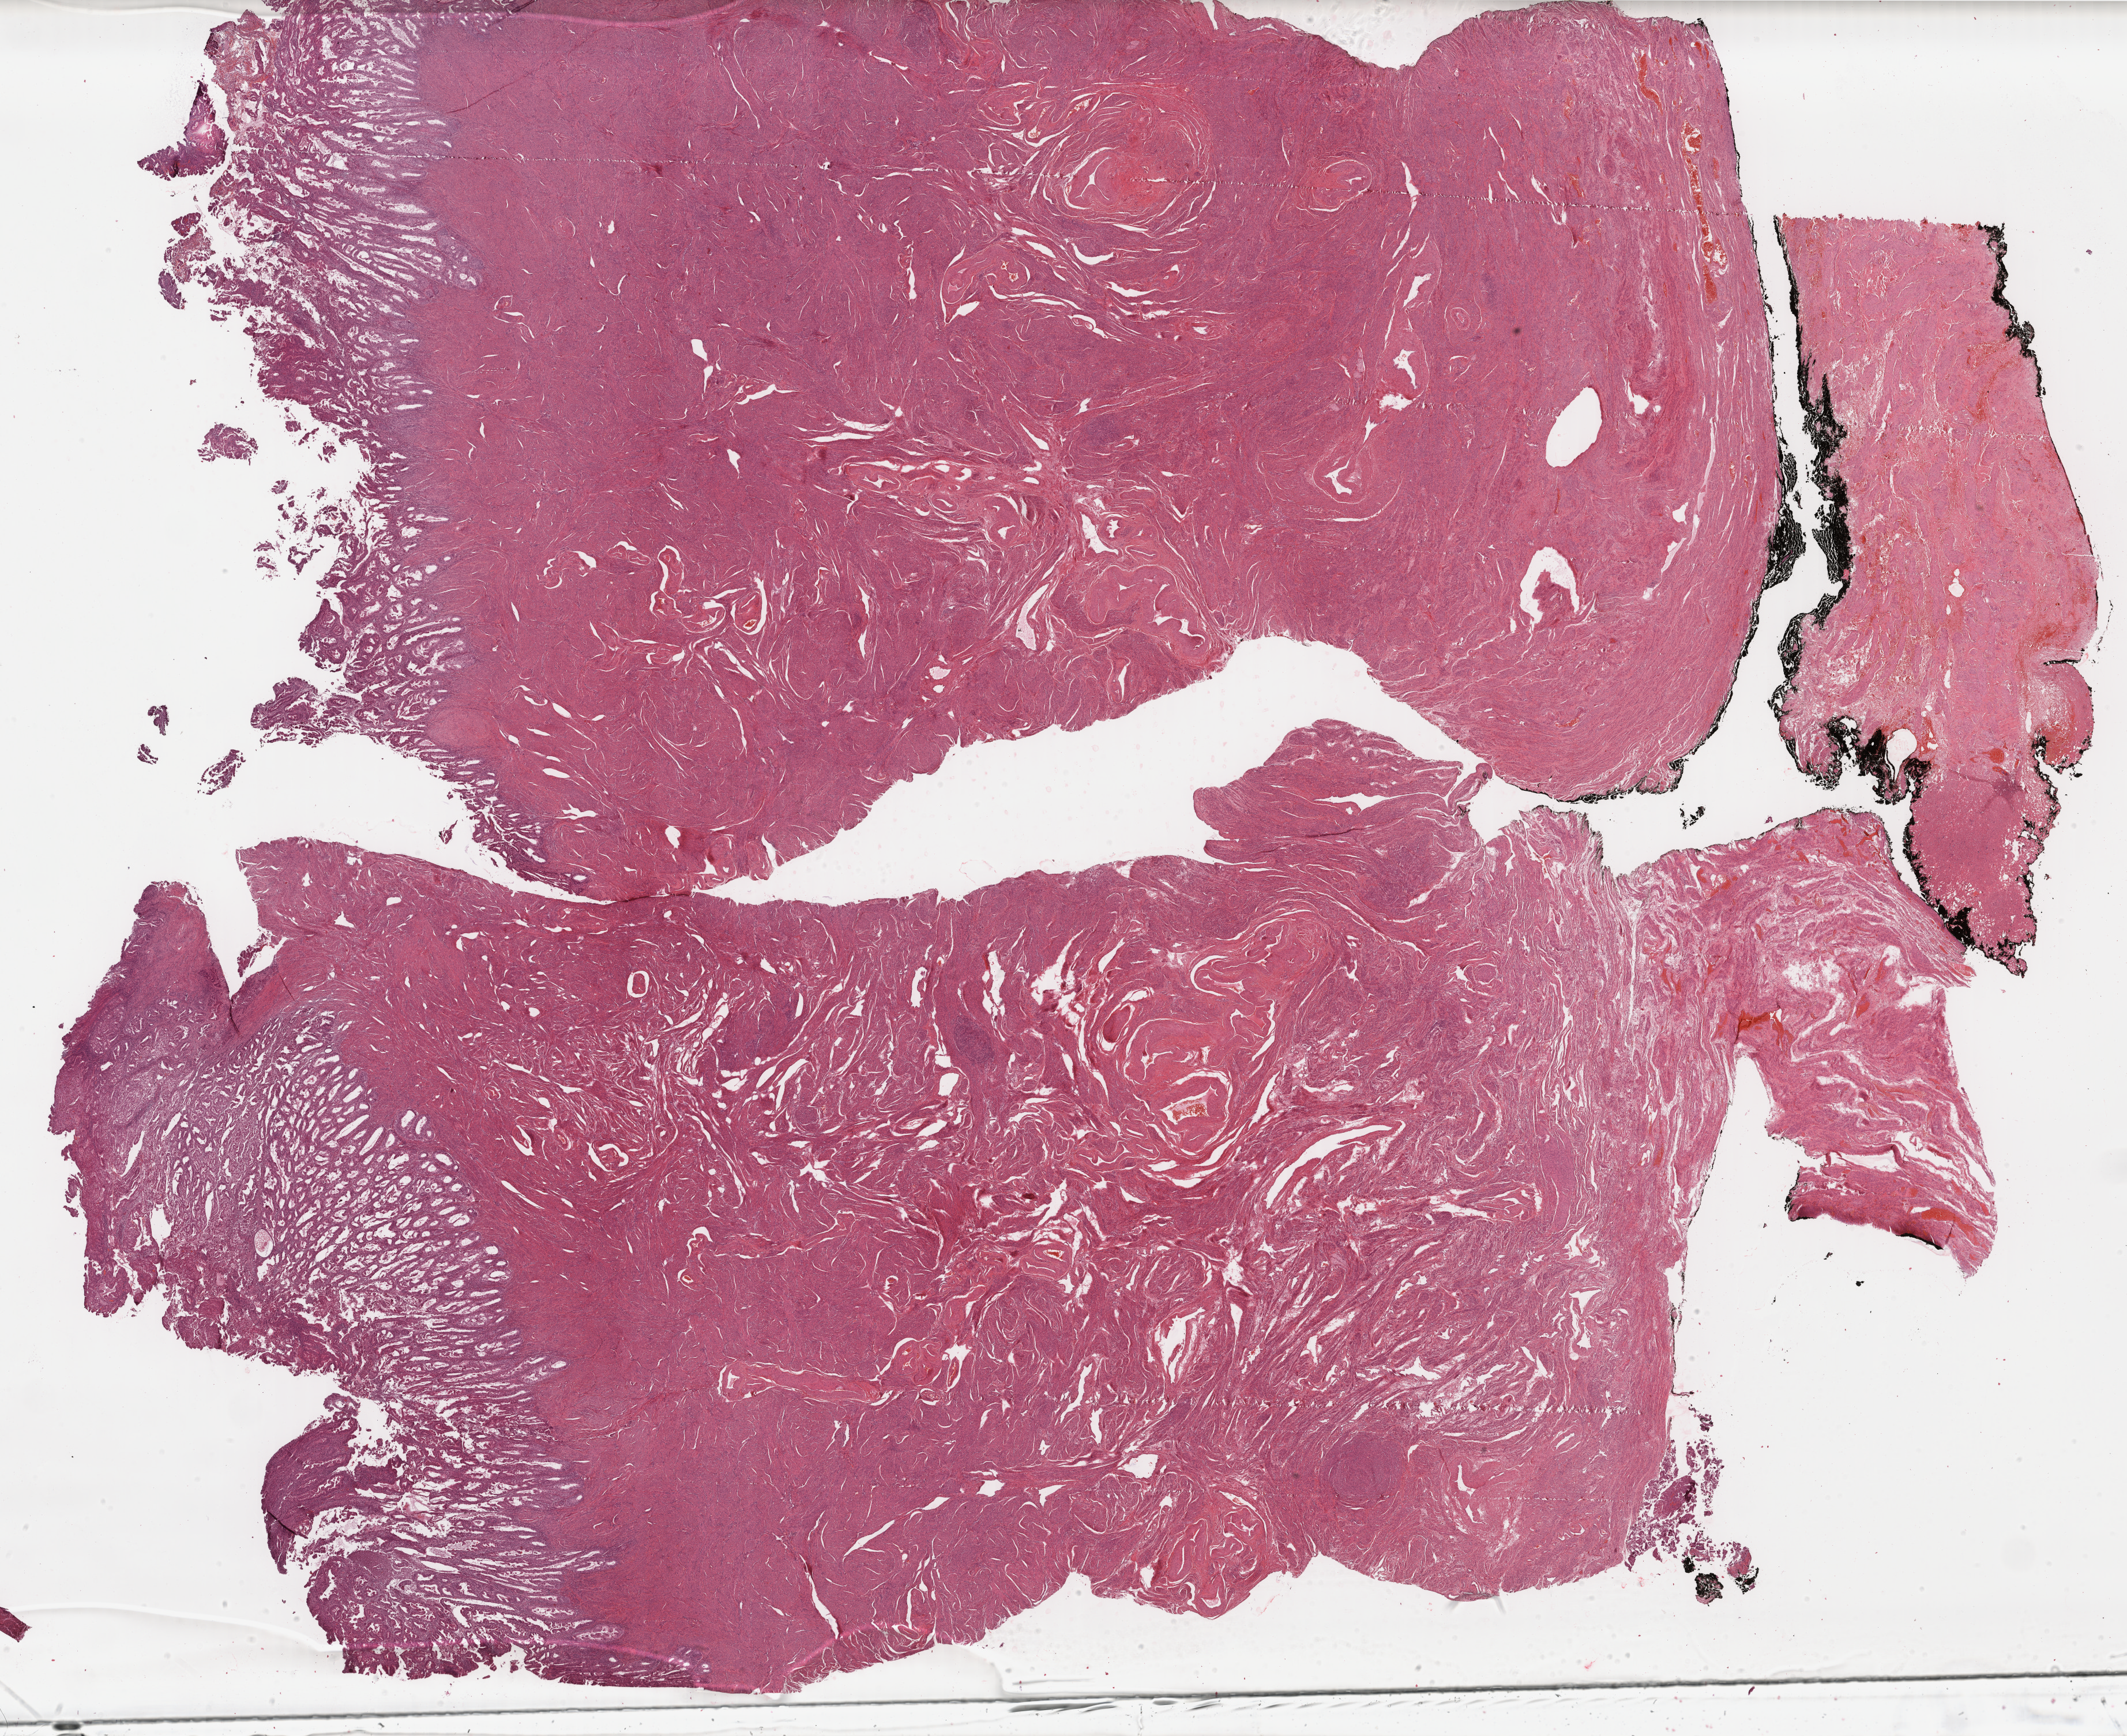
Whole-slide histology image, H&E-stained, a low-resolution overview of the entire scanned area, about 29.3 x 23.9 mm (acquisition: 40x scan). Formalin-fixed paraffin-embedded (FFPE) diagnostic section. Uterus, primary tumour sample. Female patient; age at initial diagnosis 55 years. Histologic grade: G1 (well differentiated).
FIGO stage: IB. Pathologic diagnosis: Endometrioid adenocarcinoma, NOS (endometrium). Lymph nodes positive (case pathology): 0 of 8 examined.